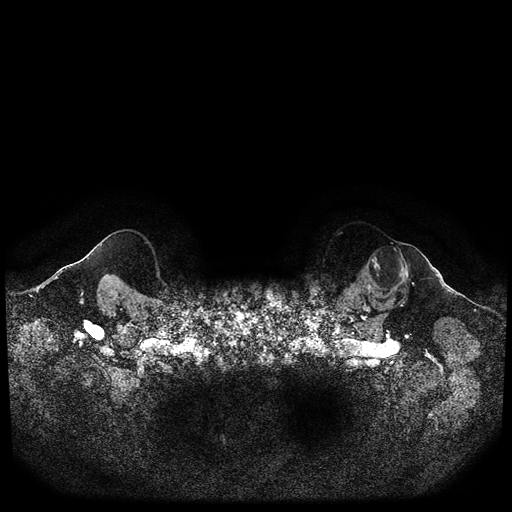
Breast MRI (dynamic contrast-enhanced, multi-phase), one axial slice. Position 97 of 116 along the scan axis. Dynamic contrast-enhanced series, time point 2 of 5 at this slice position (early post-contrast). 1.5 T. TE 2.6 ms, TR 5.3 ms. 2 mm slice thickness. 512 × 512 image matrix. Female patient, age 64 years.
Structures marked on this image (semi-automatically segmented with operator editing):
- breast lesion (labelled 'tumour' in the annotation; benign lesions carry a separate 'benign' label): box from (x=358, y=242) to (x=410, y=300) px